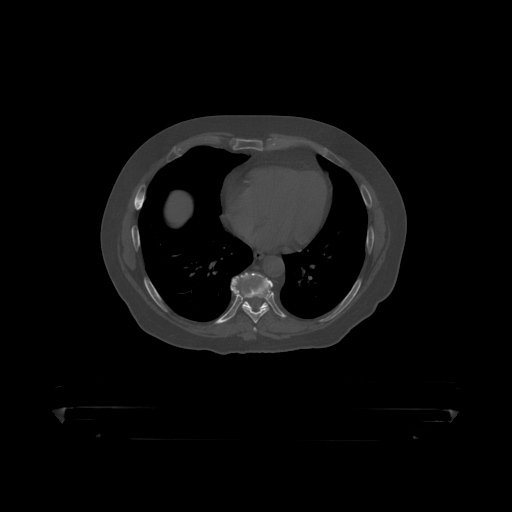
CT including the spine, one axial slice; slice 251 of 390 in the series (ordered by position); 120 kVp; bone window (W 1800 / L 400 HU); 512 × 512 image matrix, field of view 650 × 650 mm. Patient: male, 60 years. From the clinical record (not read from this slice): primary cancer: prostate.
Structures marked on this image (semi-automatically segmented with operator editing):
- T8 vertebra: box from (x=233, y=279) to (x=273, y=319) px
- T9 vertebra: (x=231, y=273)–(x=268, y=309)